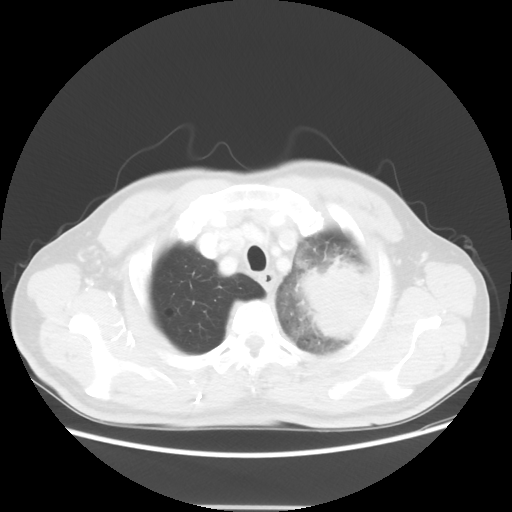
Chest CT, one axial slice. Position 49 of 53 along the scan axis. Reconstruction kernel STANDARD. 100 kVp. Lung window (W 1500 / L -600 HU). 5 mm slice thickness. 512 × 512 image matrix, field of view 391 × 391 mm. Patient: male, 60 years. From the clinical record (not read from this slice): clinical TNM (as recorded): T4 N1 M1a.
Structures marked on this image (rectangle marked by the reading radiologist):
- lung tumour (recorded histology: large cell carcinoma): bounding box <287,248,377,339> (left, top, right, bottom; pixels)